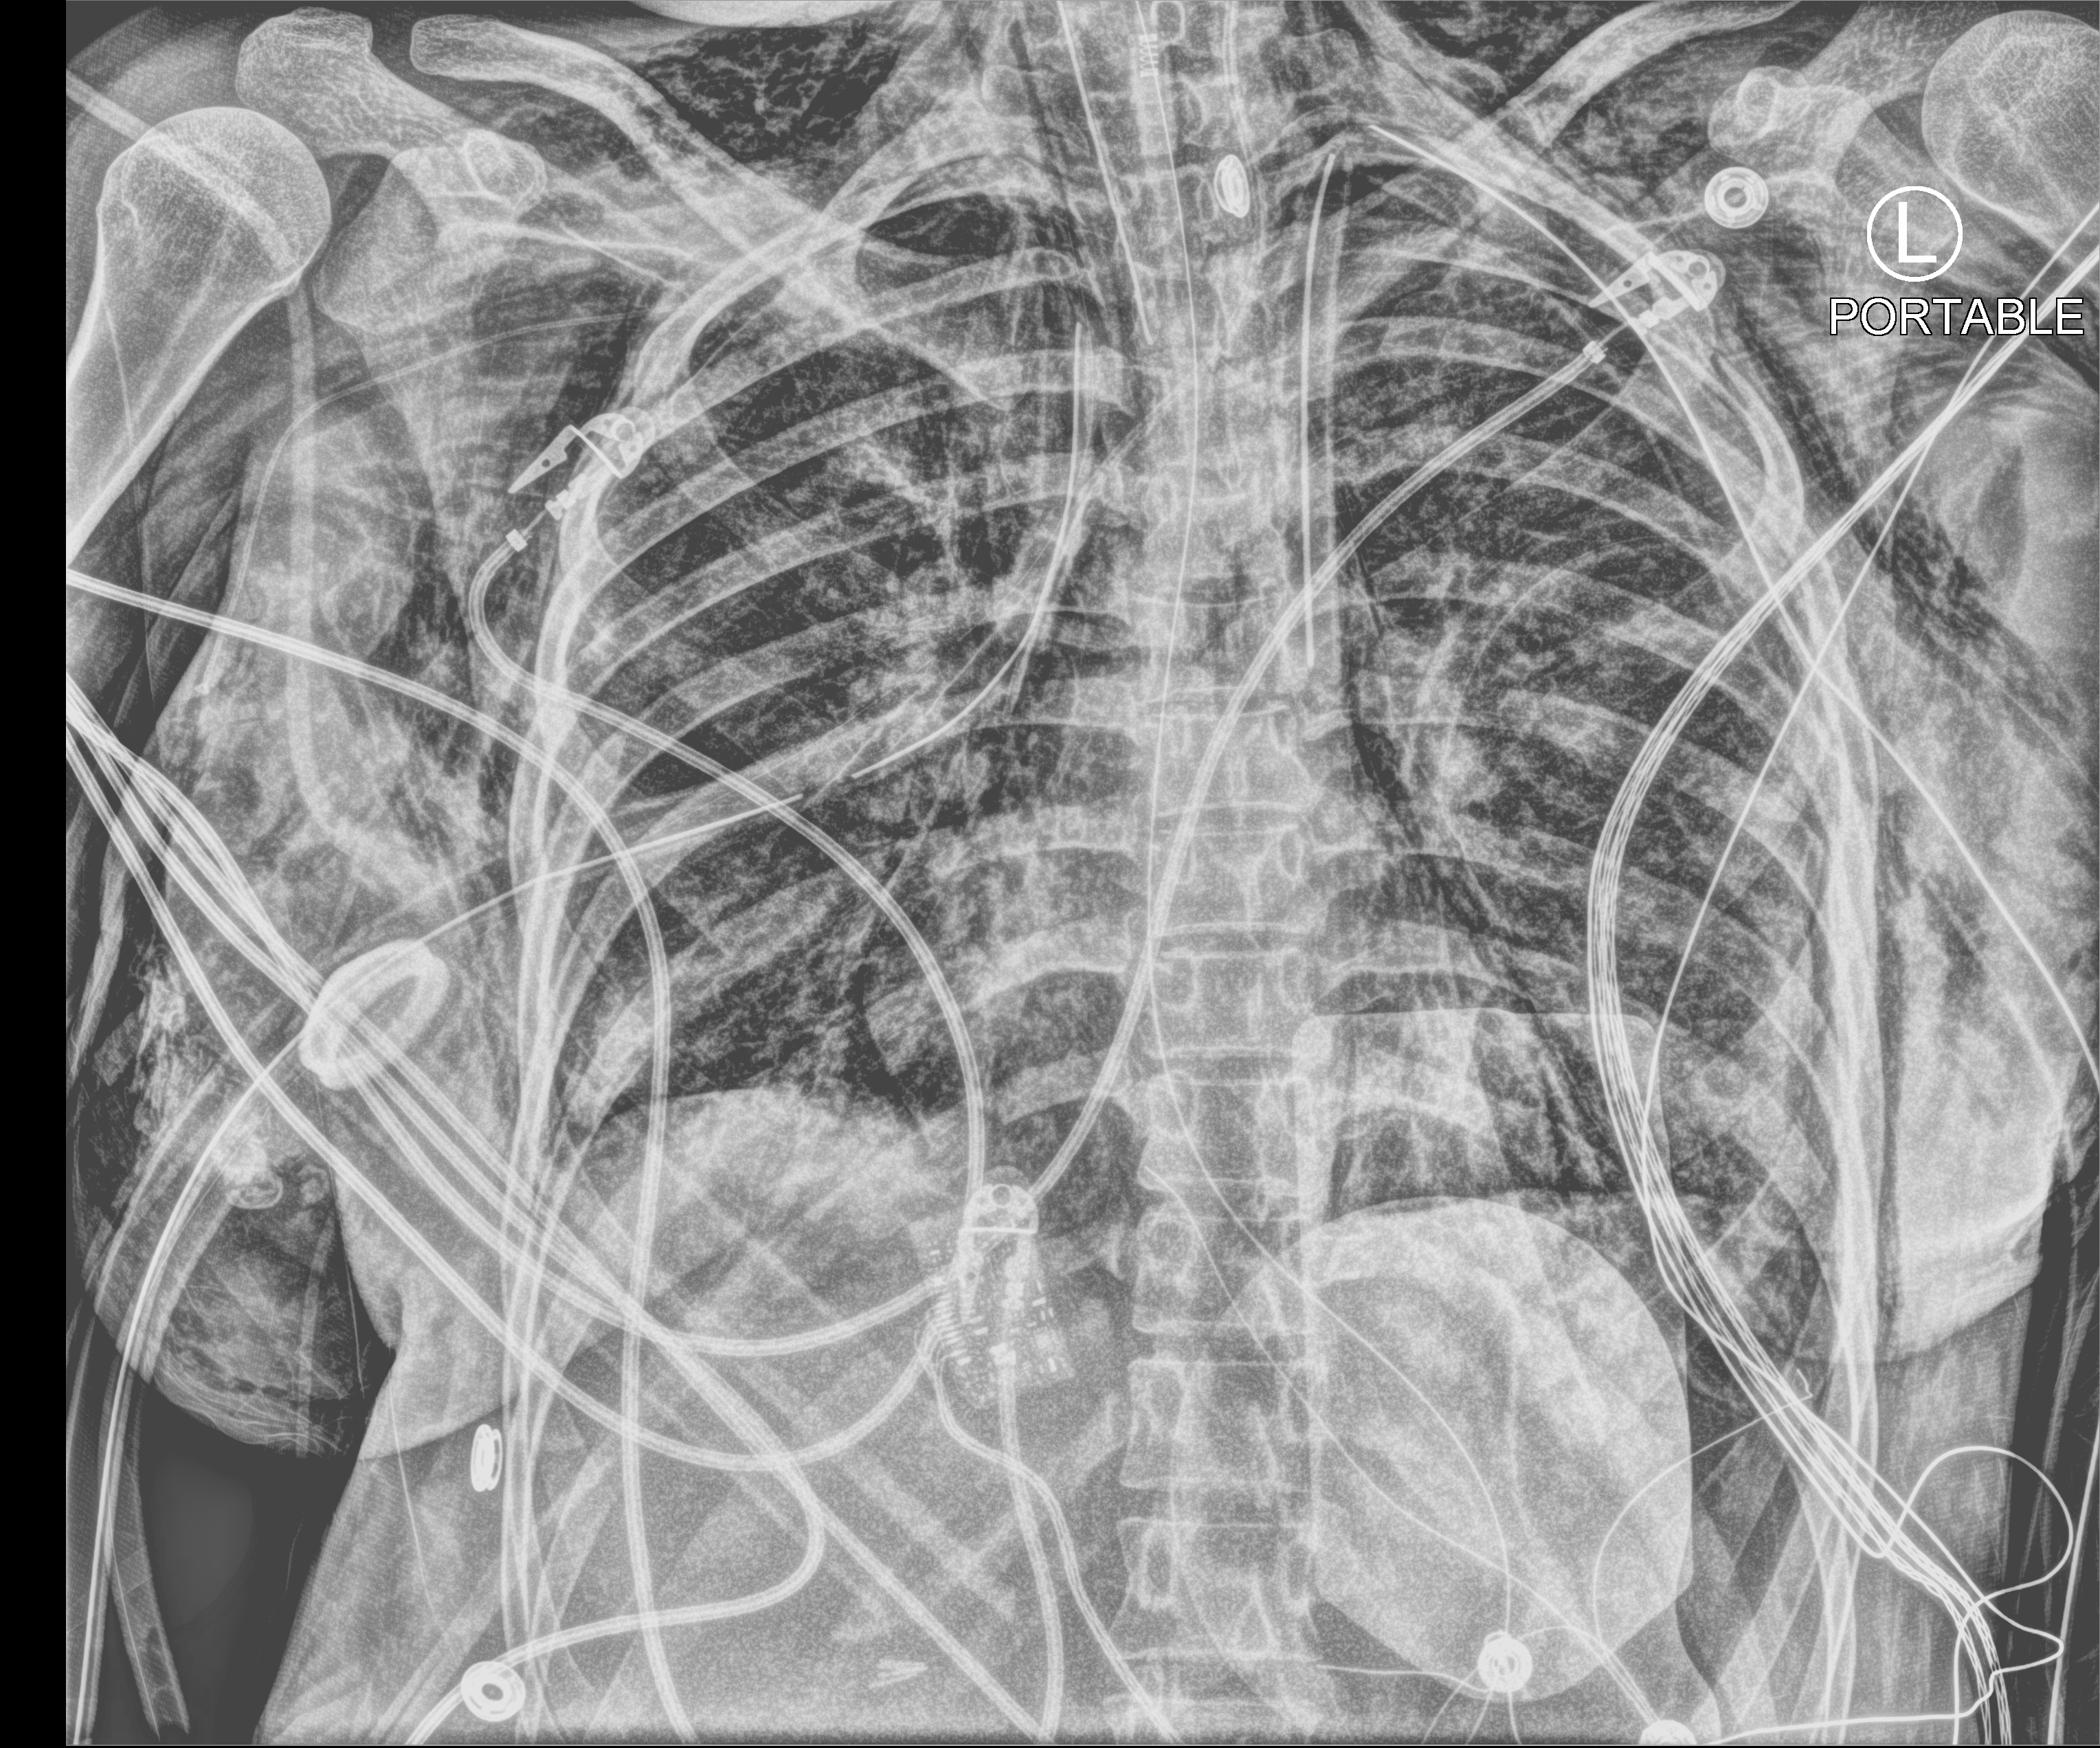
Chest X-ray (portable); anteroposterior (AP) projection. Patient hospitalised with COVID-19, aged 18–59 years.
Admission-level facts for this patient (not findings on this image; timing relative to this image not recorded):
- other chronic lung disease (admission record): no
- chronic kidney disease (admission record): no